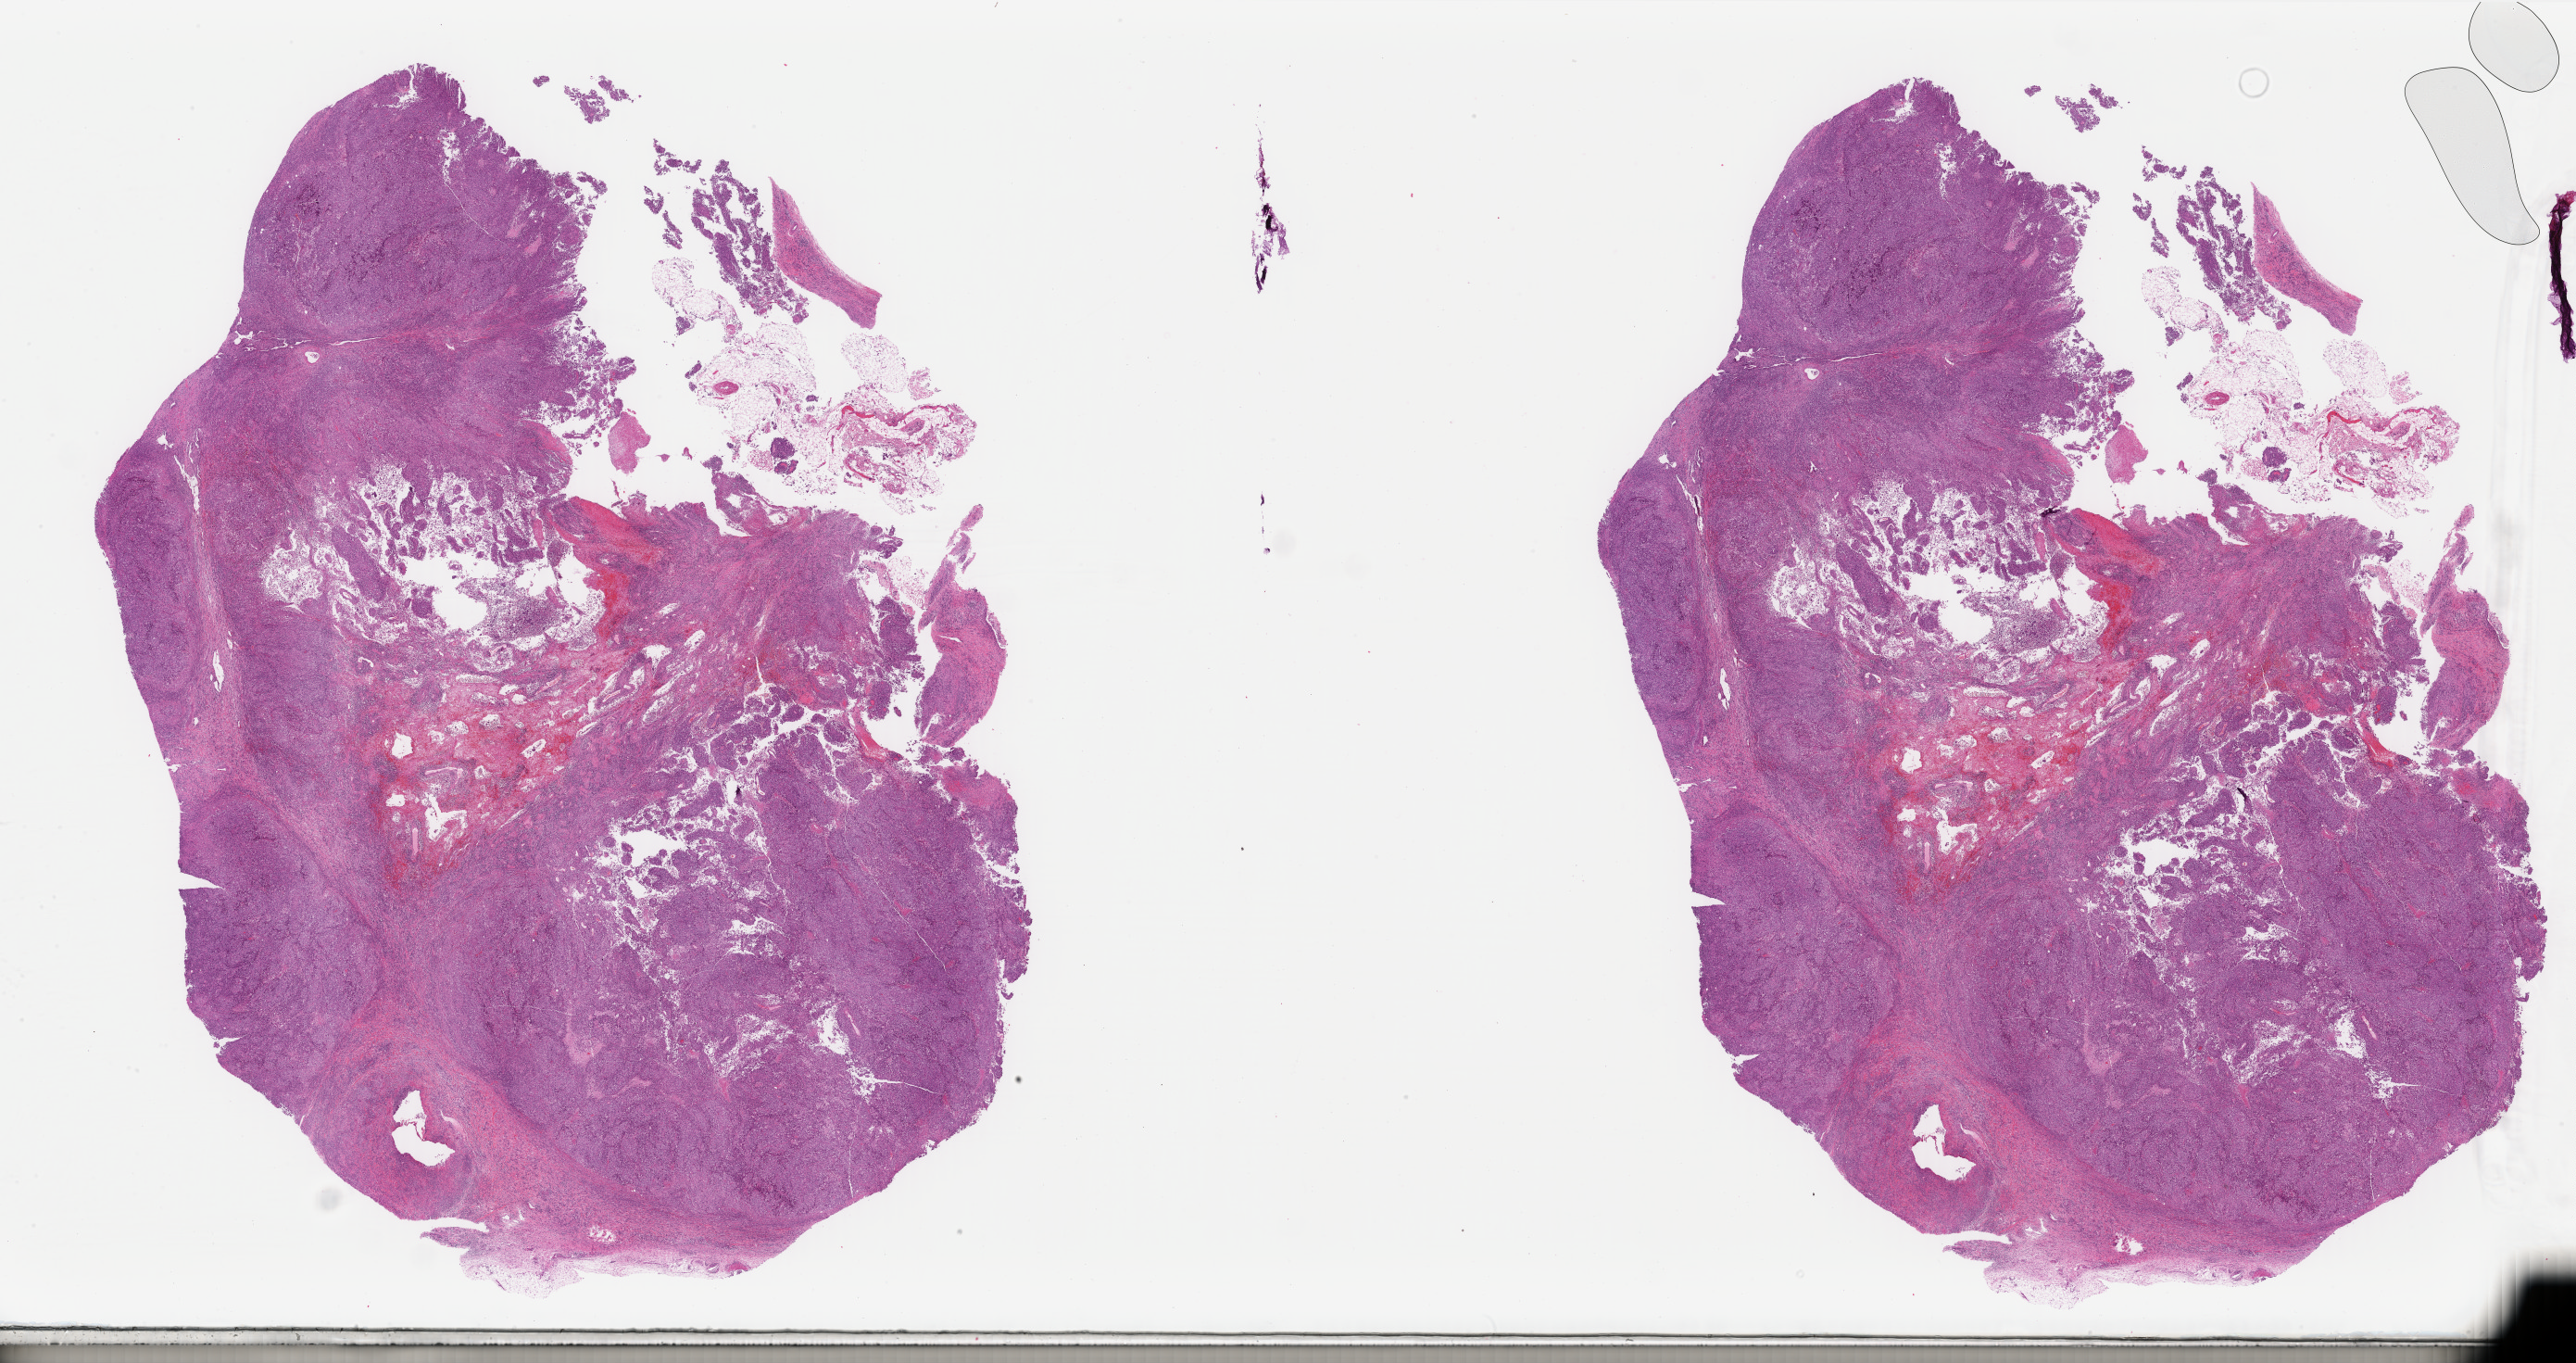
Digitized Hematoxylin and eosin (H&E) stained tissue section (whole slide), shown as a low-resolution overview of the whole scanned area (about 44.1 x 23.4 mm). Formalin-fixed paraffin-embedded (FFPE) diagnostic section. Primary tumour sample from the skin. Female patient; age at initial diagnosis 48 years.
- pathologic diagnosis: Malignant melanoma, NOS